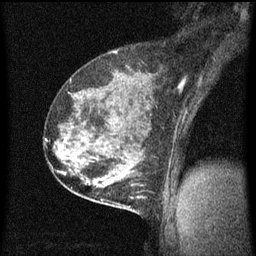
Breast MRI (dynamic contrast-enhanced), one sagittal slice. Position 41 of 60 along the scan axis. Dynamic contrast-enhanced series, image 2 of 3 at this slice position (ordered by acquisition). 1.5 T. TE 4.2 ms, TR 8 ms. 2 mm slice thickness. 256 × 256 image matrix, field of view 180 × 180 mm. Female patient, age 35 years.
Annotated regions visible in this slice (semi-automatic segmentation, software-assisted and operator-edited):
- analysis volume of interest (the breast-tissue region the enhancement analysis was run in; not a lesion): bounding box (x1, y1, x2, y2) in pixels: (110, 178, 154, 215)
- tumour enhancement mask (voxels above the 70 % enhancement threshold inside the analysis volume of interest): (110, 178, 145, 207)